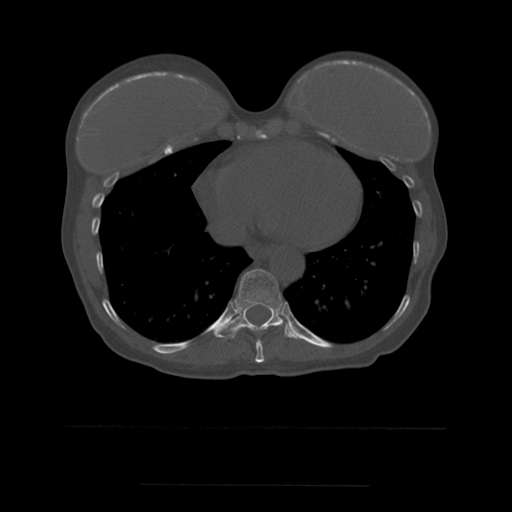
CT including the spine, one axial slice. Slice 308 of 544 in the series (ordered by position). Bone window (W 1800 / L 400 HU). 512 × 512 image matrix, field of view 350 × 350 mm. Patient age 58 years. Case-level facts recorded for this patient, not image findings: primary cancer: lung.
Structures marked on this image (semi-automatically segmented with operator editing):
- T10 vertebra: bounding box [x1, y1, x2, y2] px = [216, 269, 299, 339]
- T9 vertebra: [255, 340, 265, 363]